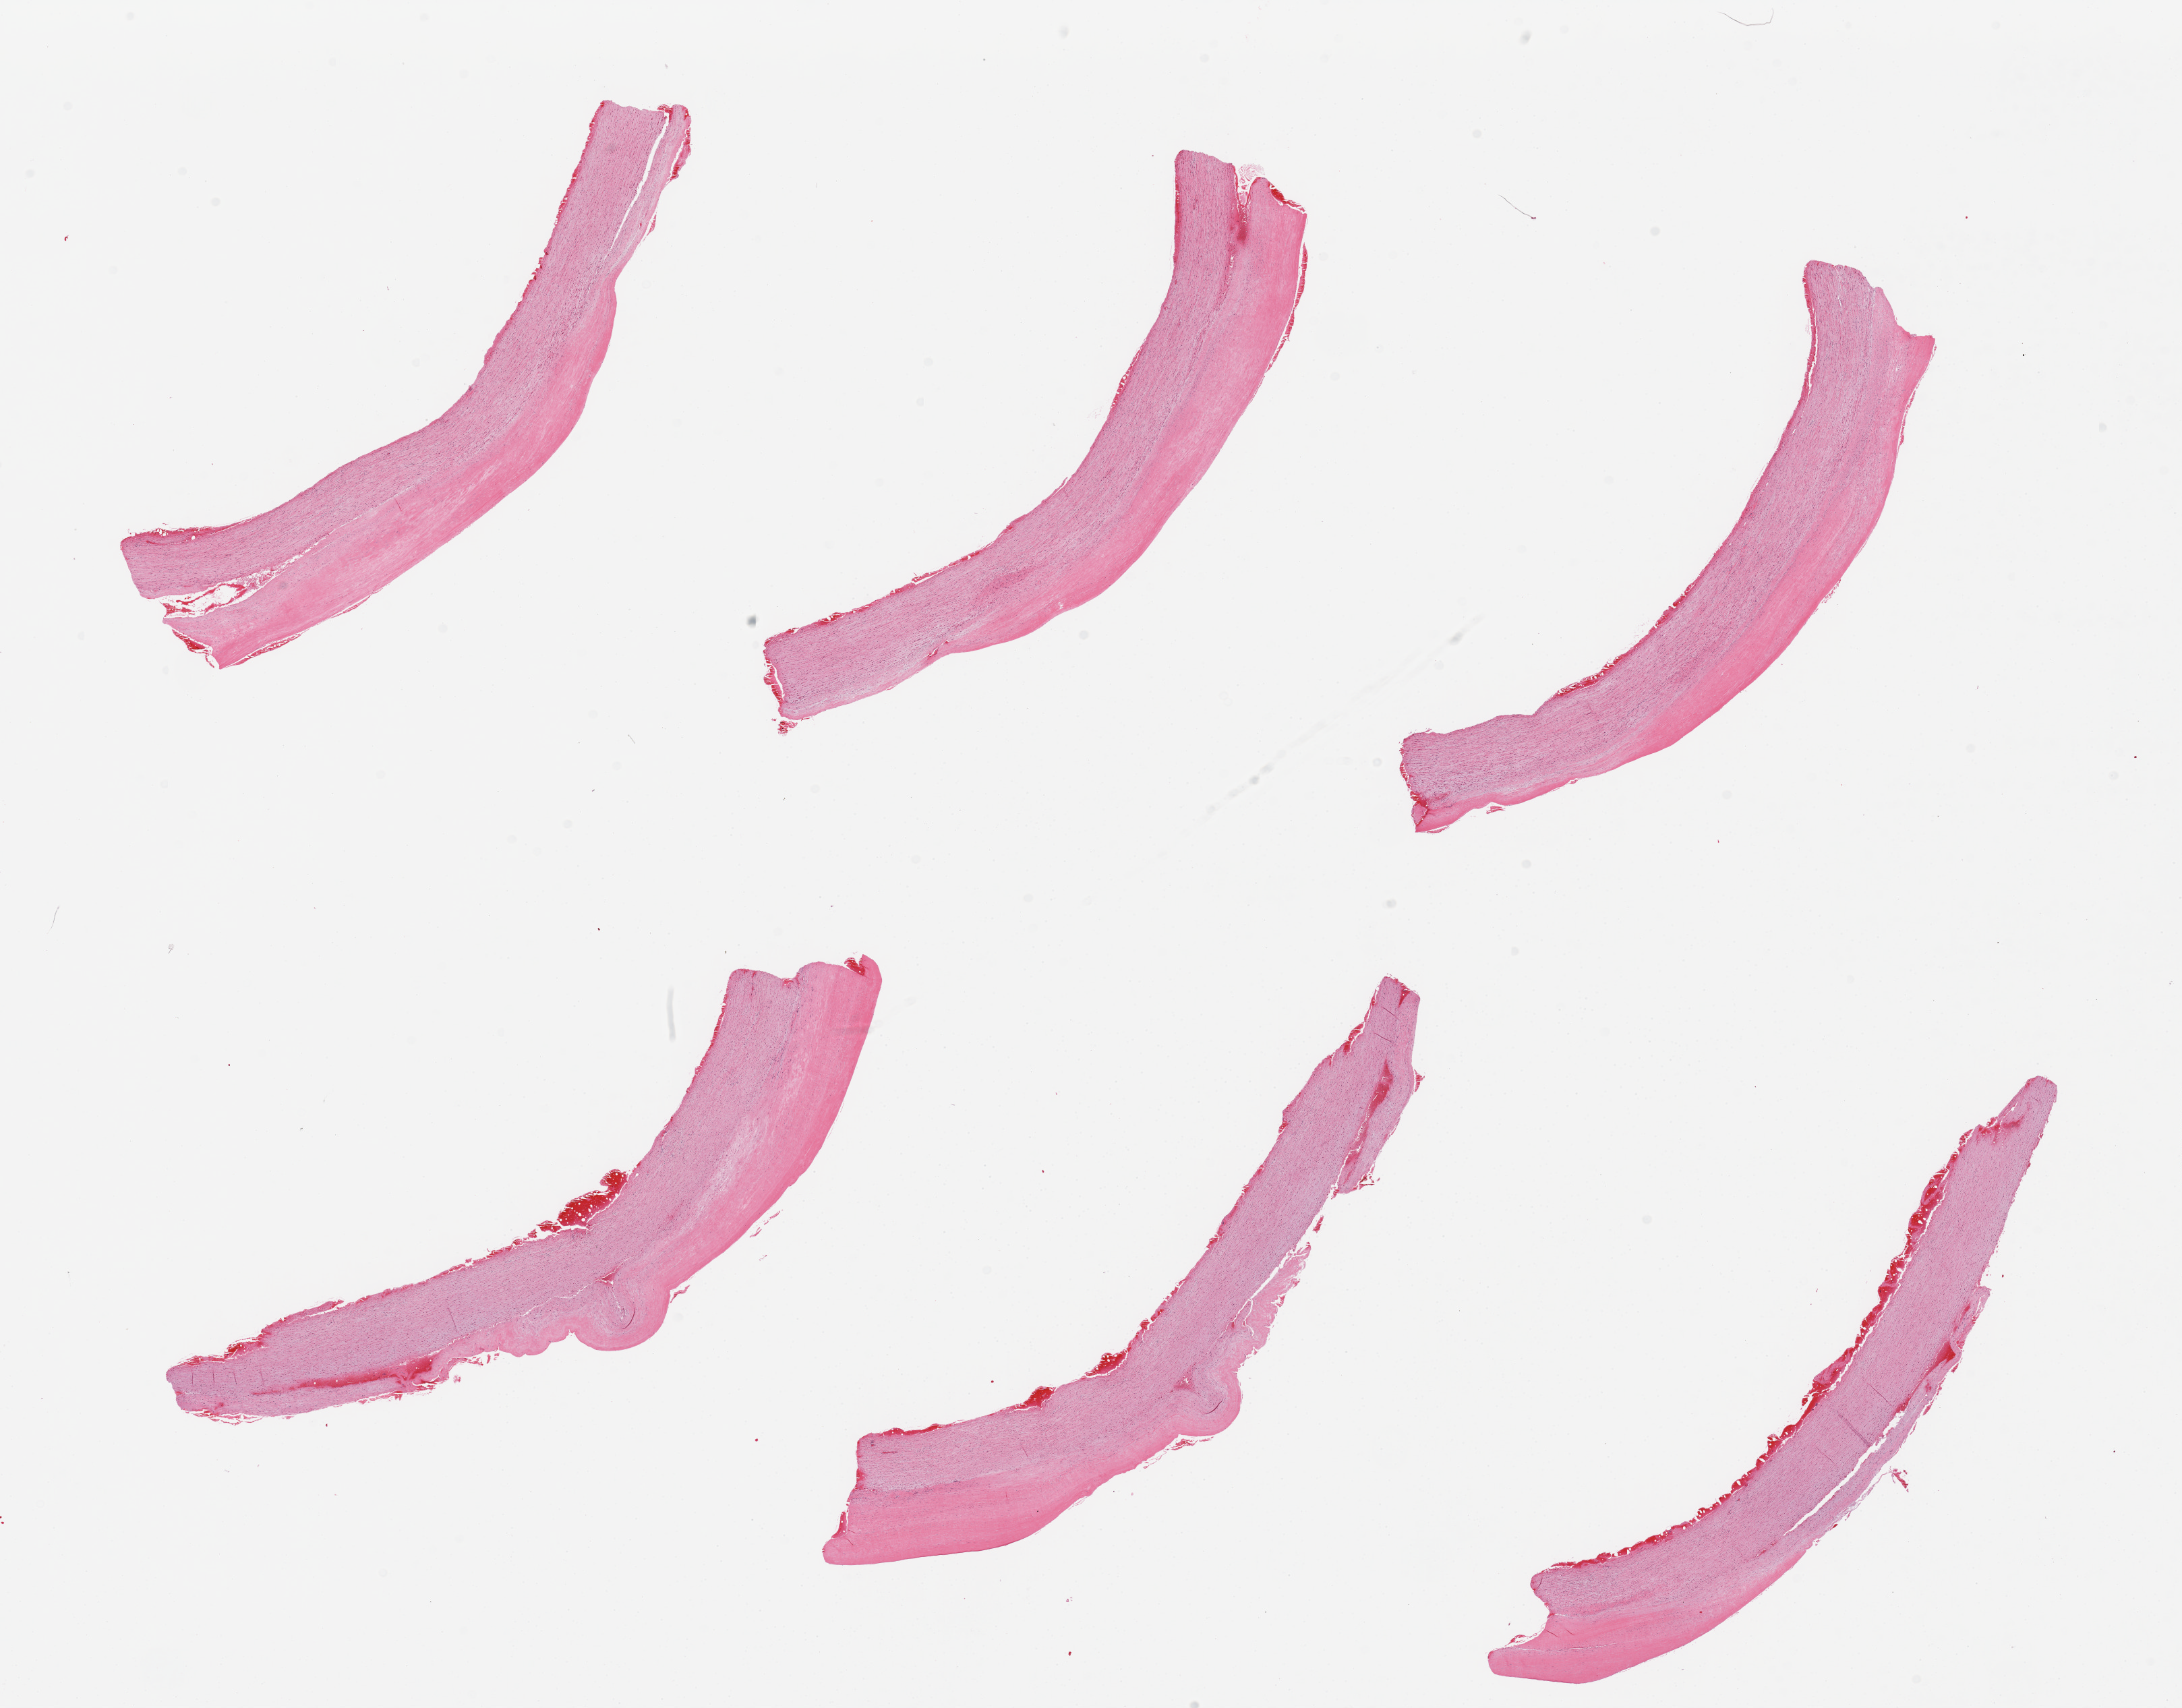
Hematoxylin and eosin (H&E) whole-slide image — a low-resolution overview of the entire scanned area, about 25.6 x 20.0 mm (acquisition: 20x scan); PAXgene-fixed, paraffin-embedded tissue; target tissue: aorta; tissue donor sample.
Pathologist's review note for this sample: 6 pieces, atherosclerosis.